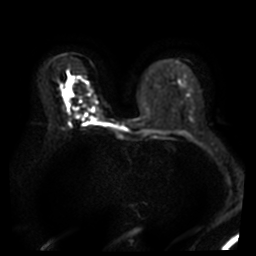
Breast MRI, one axial slice; slice 22 of 46 in the series (ordered by position); diffusion-weighted series; image 2 of 4 stored at this slice position (different b-values; order by instance number); 3 T; 5 mm slice thickness; 256 × 256 image matrix, field of view 340 × 340 mm. Female patient.
Structures marked on this image (outlined manually by an expert reader):
- tumour on diffusion-weighted imaging: bounding box [x1, y1, x2, y2] px = [92, 107, 95, 111]